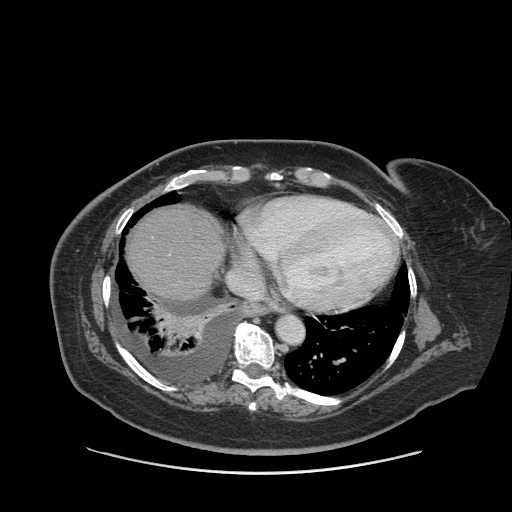
Contrast-enhanced abdominal CT (liver protocol), one axial slice. Slice 79 of 91 in the series (ordered by position). 140 kVp. Soft-tissue window (W 400 / L 40 HU). 2.5 mm slice thickness. 512 × 512 image matrix, field of view 420 × 420 mm. From the clinical record (not read from this slice): diagnosis: hepatocellular carcinoma (patient treated with transarterial chemoembolisation; whether this scan precedes or follows treatment is not stated here); TNM stage (as recorded): Stage-I; Child-Pugh class: A; tumour differentiation: well differentiated.
Outlined on this slice (semi-automatically segmented with operator editing):
- abdominal aorta: bounding box <277,316,304,343> (left, top, right, bottom; pixels)
- liver parenchyma outside the tumour (the mass and vessels are separate outlines, so this box may not span the whole liver): <126,206,224,298>